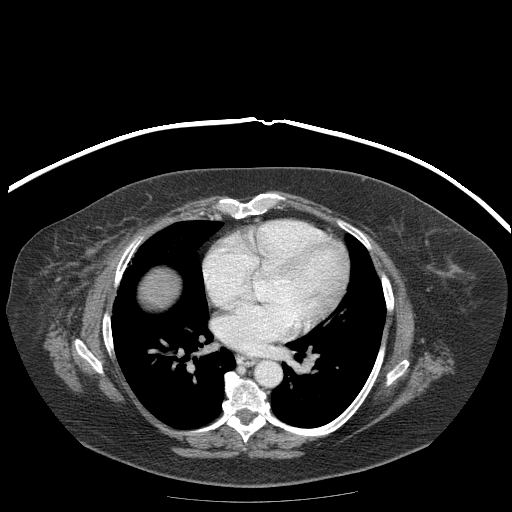
Contrast-enhanced abdominal CT (liver protocol), one axial slice. Position 191 of 204 along the scan axis. Reconstruction kernel STANDARD. Soft-tissue window (W 400 / L 40 HU). 2.5 mm slice thickness. 512 × 512 image matrix, field of view 440 × 440 mm. Case-level facts recorded for this patient, not image findings: diagnosis: hepatocellular carcinoma (patient treated with transarterial chemoembolisation; whether this scan precedes or follows treatment is not stated here); TNM stage (as recorded): Stage-IIIB; Child-Pugh class: A; tumour differentiation: well differentiated; tumour nodularity: uninodular.
Structures marked on this image (semi-automatically segmented with operator editing):
- liver parenchyma outside the tumour (the mass and vessels are separate outlines, so this box may not span the whole liver): box from (x=140, y=268) to (x=178, y=306) px